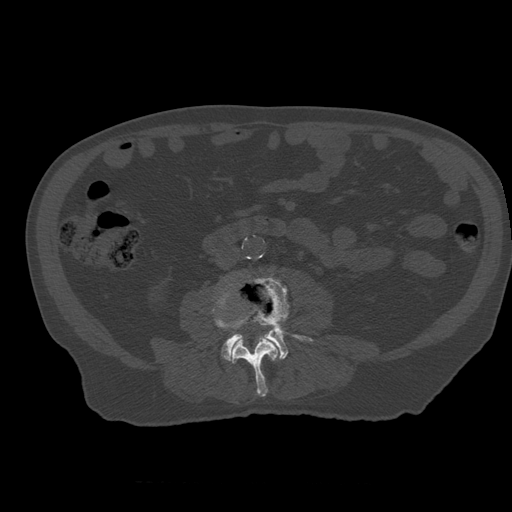
CT including the spine, one axial slice. Reconstruction kernel STANDARD. Bone window (W 1800 / L 400 HU). 512 × 512 image matrix, field of view 407 × 407 mm. Patient age 73 years. From the clinical record (not read from this slice): primary cancer: prostate; vertebrae with lytic lesions (as recorded): L2.
Outlined on this slice (semi-automatically segmented with operator editing):
- L3 vertebra: bounding box <212,284,281,397> (left, top, right, bottom; pixels)
- L4 vertebra: <222,278,313,362>